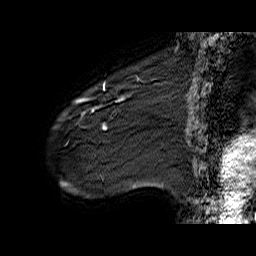
Breast MRI (dynamic contrast-enhanced), one sagittal slice; slice 11 of 60 in the series (ordered by position); dynamic contrast-enhanced series, time point 2 of 6 at this slice position (early post-contrast); 1.5 T; TE 6.4 ms, TR 32.9 ms; 4 mm slice thickness; 256 × 256 image matrix, field of view 200 × 200 mm. Female patient. From the clinical record (not read from this slice): setting: breast cancer imaged before/during neoadjuvant chemotherapy; receptor status: HER2-positive.
Structures marked on this image (semi-automatic segmentation, software-assisted and operator-edited):
- analysis volume of interest (the breast-tissue region the enhancement analysis was run in; not a lesion): bounding box (x1, y1, x2, y2) in pixels: (61, 77, 141, 142)
- tumour enhancement mask (voxels above the 100 % enhancement threshold inside the analysis volume of interest): (76, 79, 139, 129)